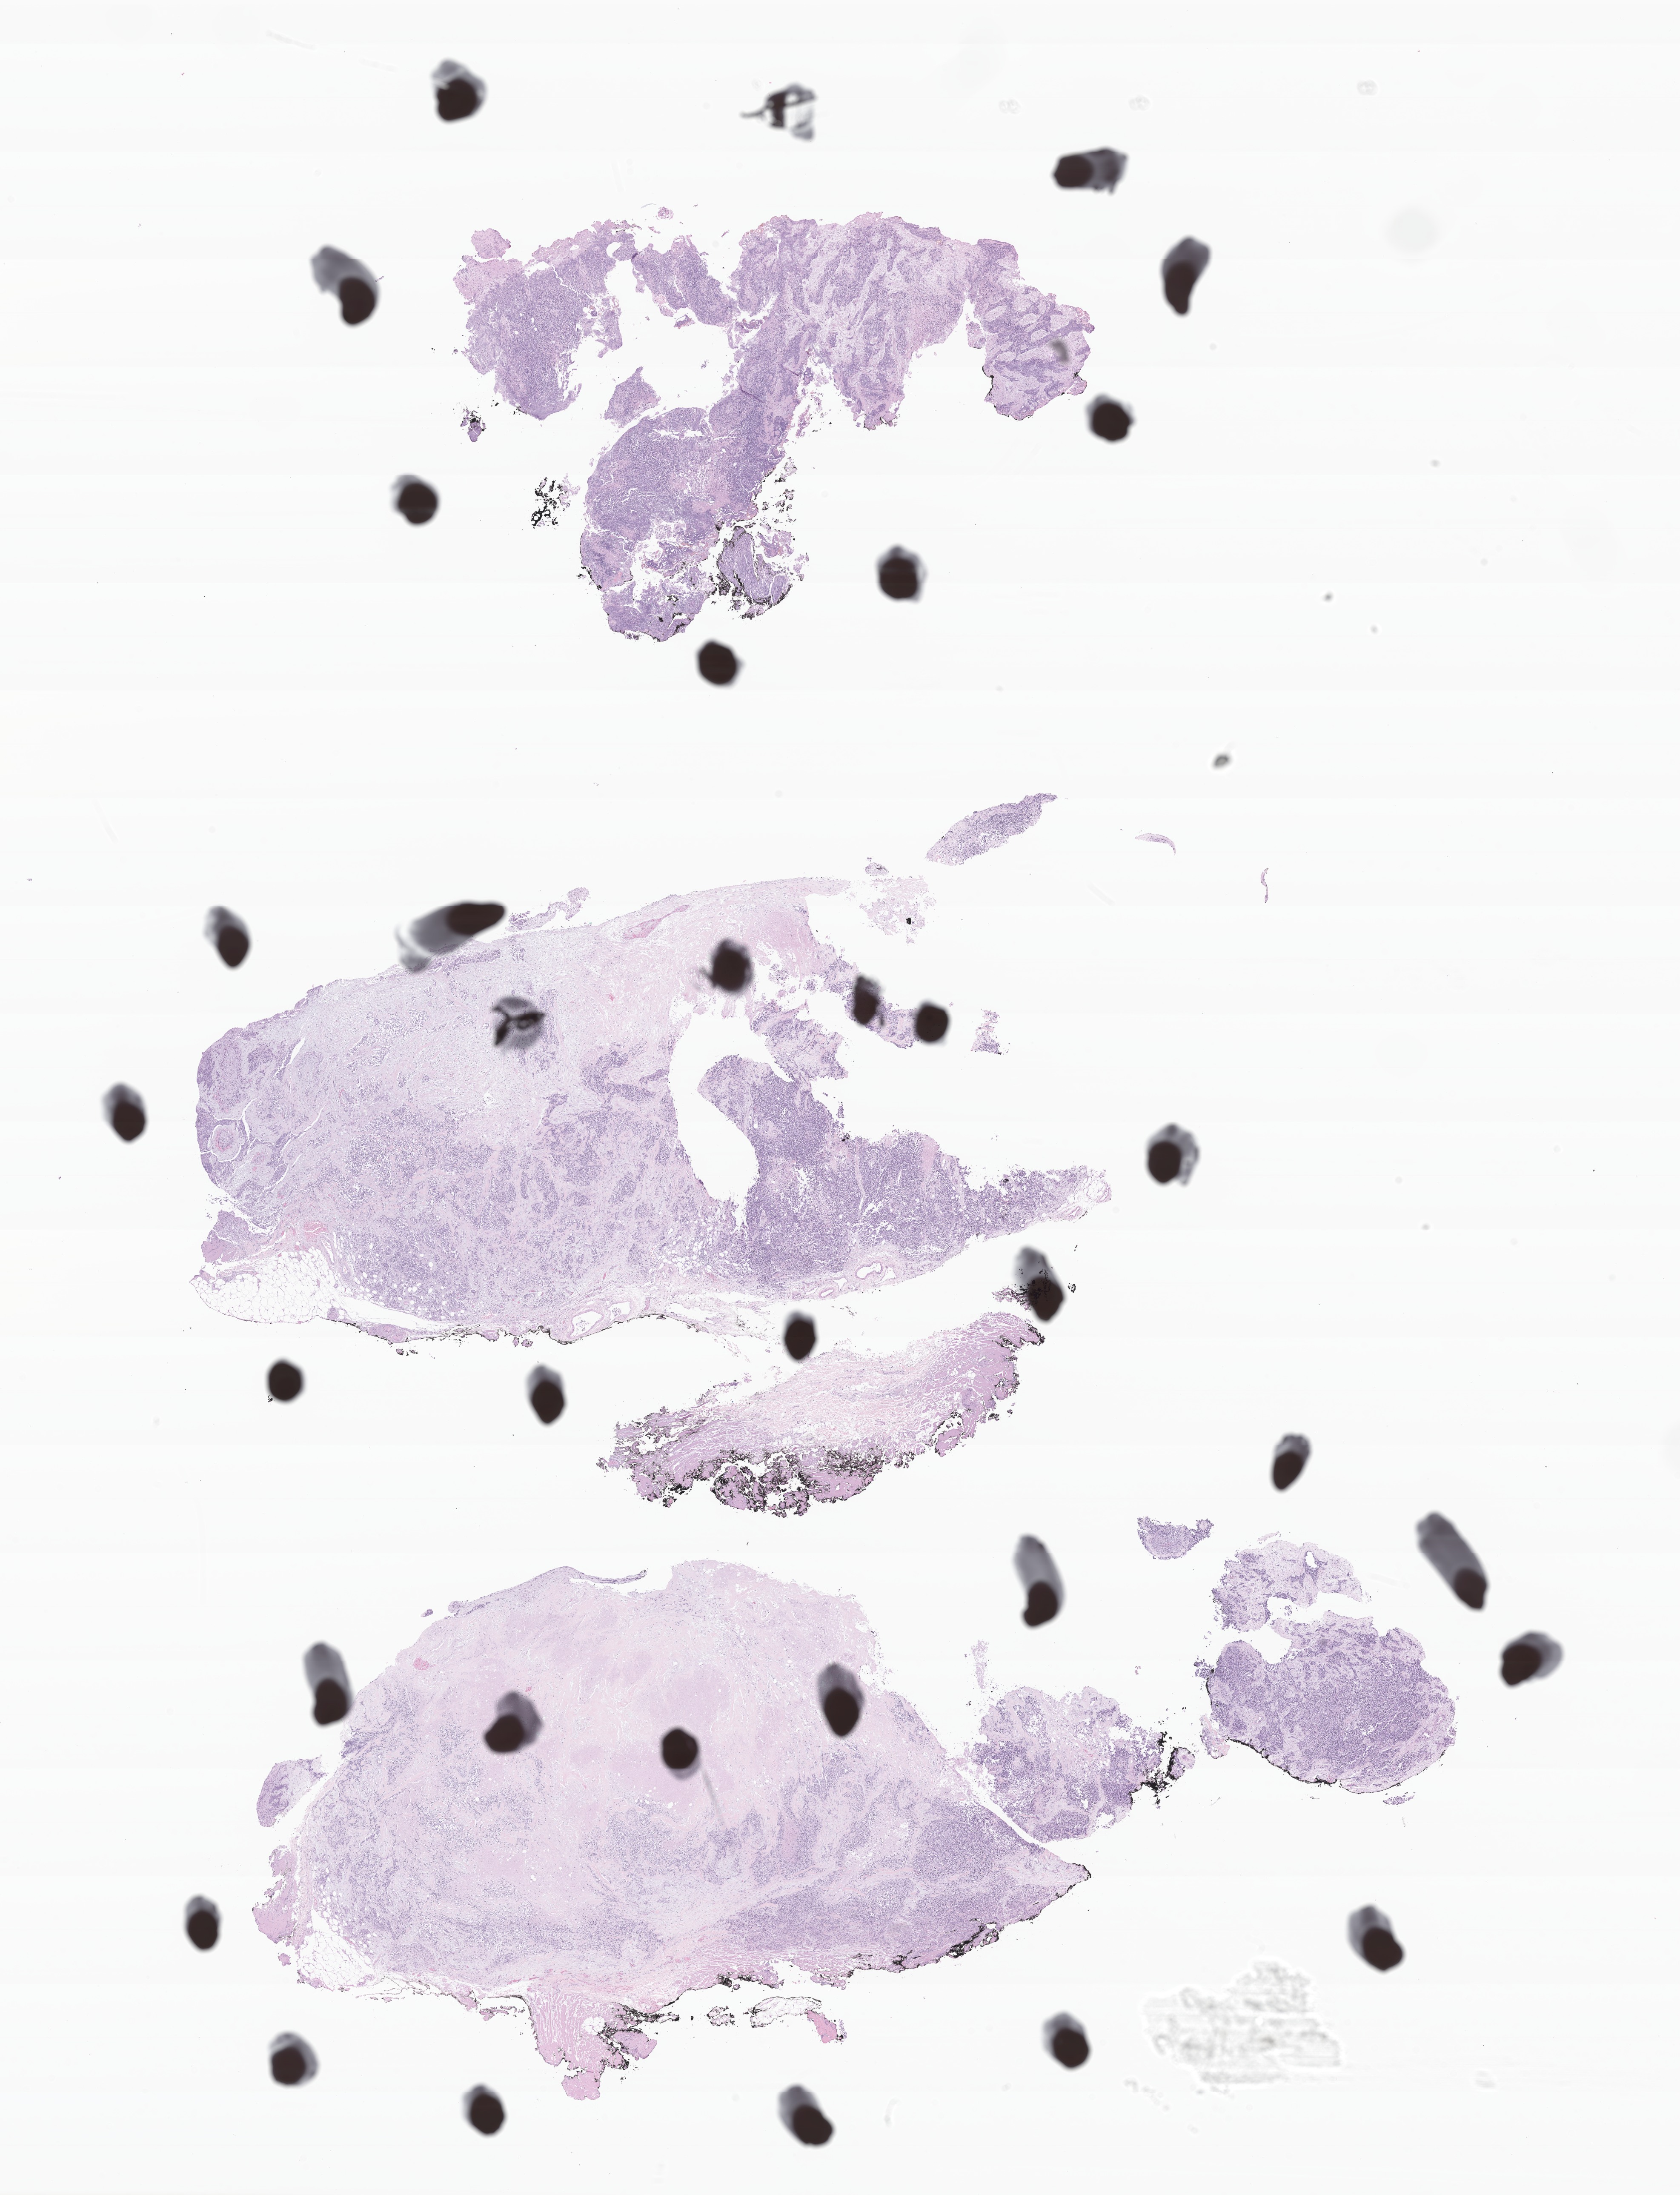
Hematoxylin and eosin (H&E) whole-slide image of tumor tissue from the peritoneum, low-resolution overview of the scanned area, about 16.6 x 21.7 mm. FFPE section. Patient female; age 137 months (11 years 5 months).
Diagnosis: Desmoplastic small round cell tumor.